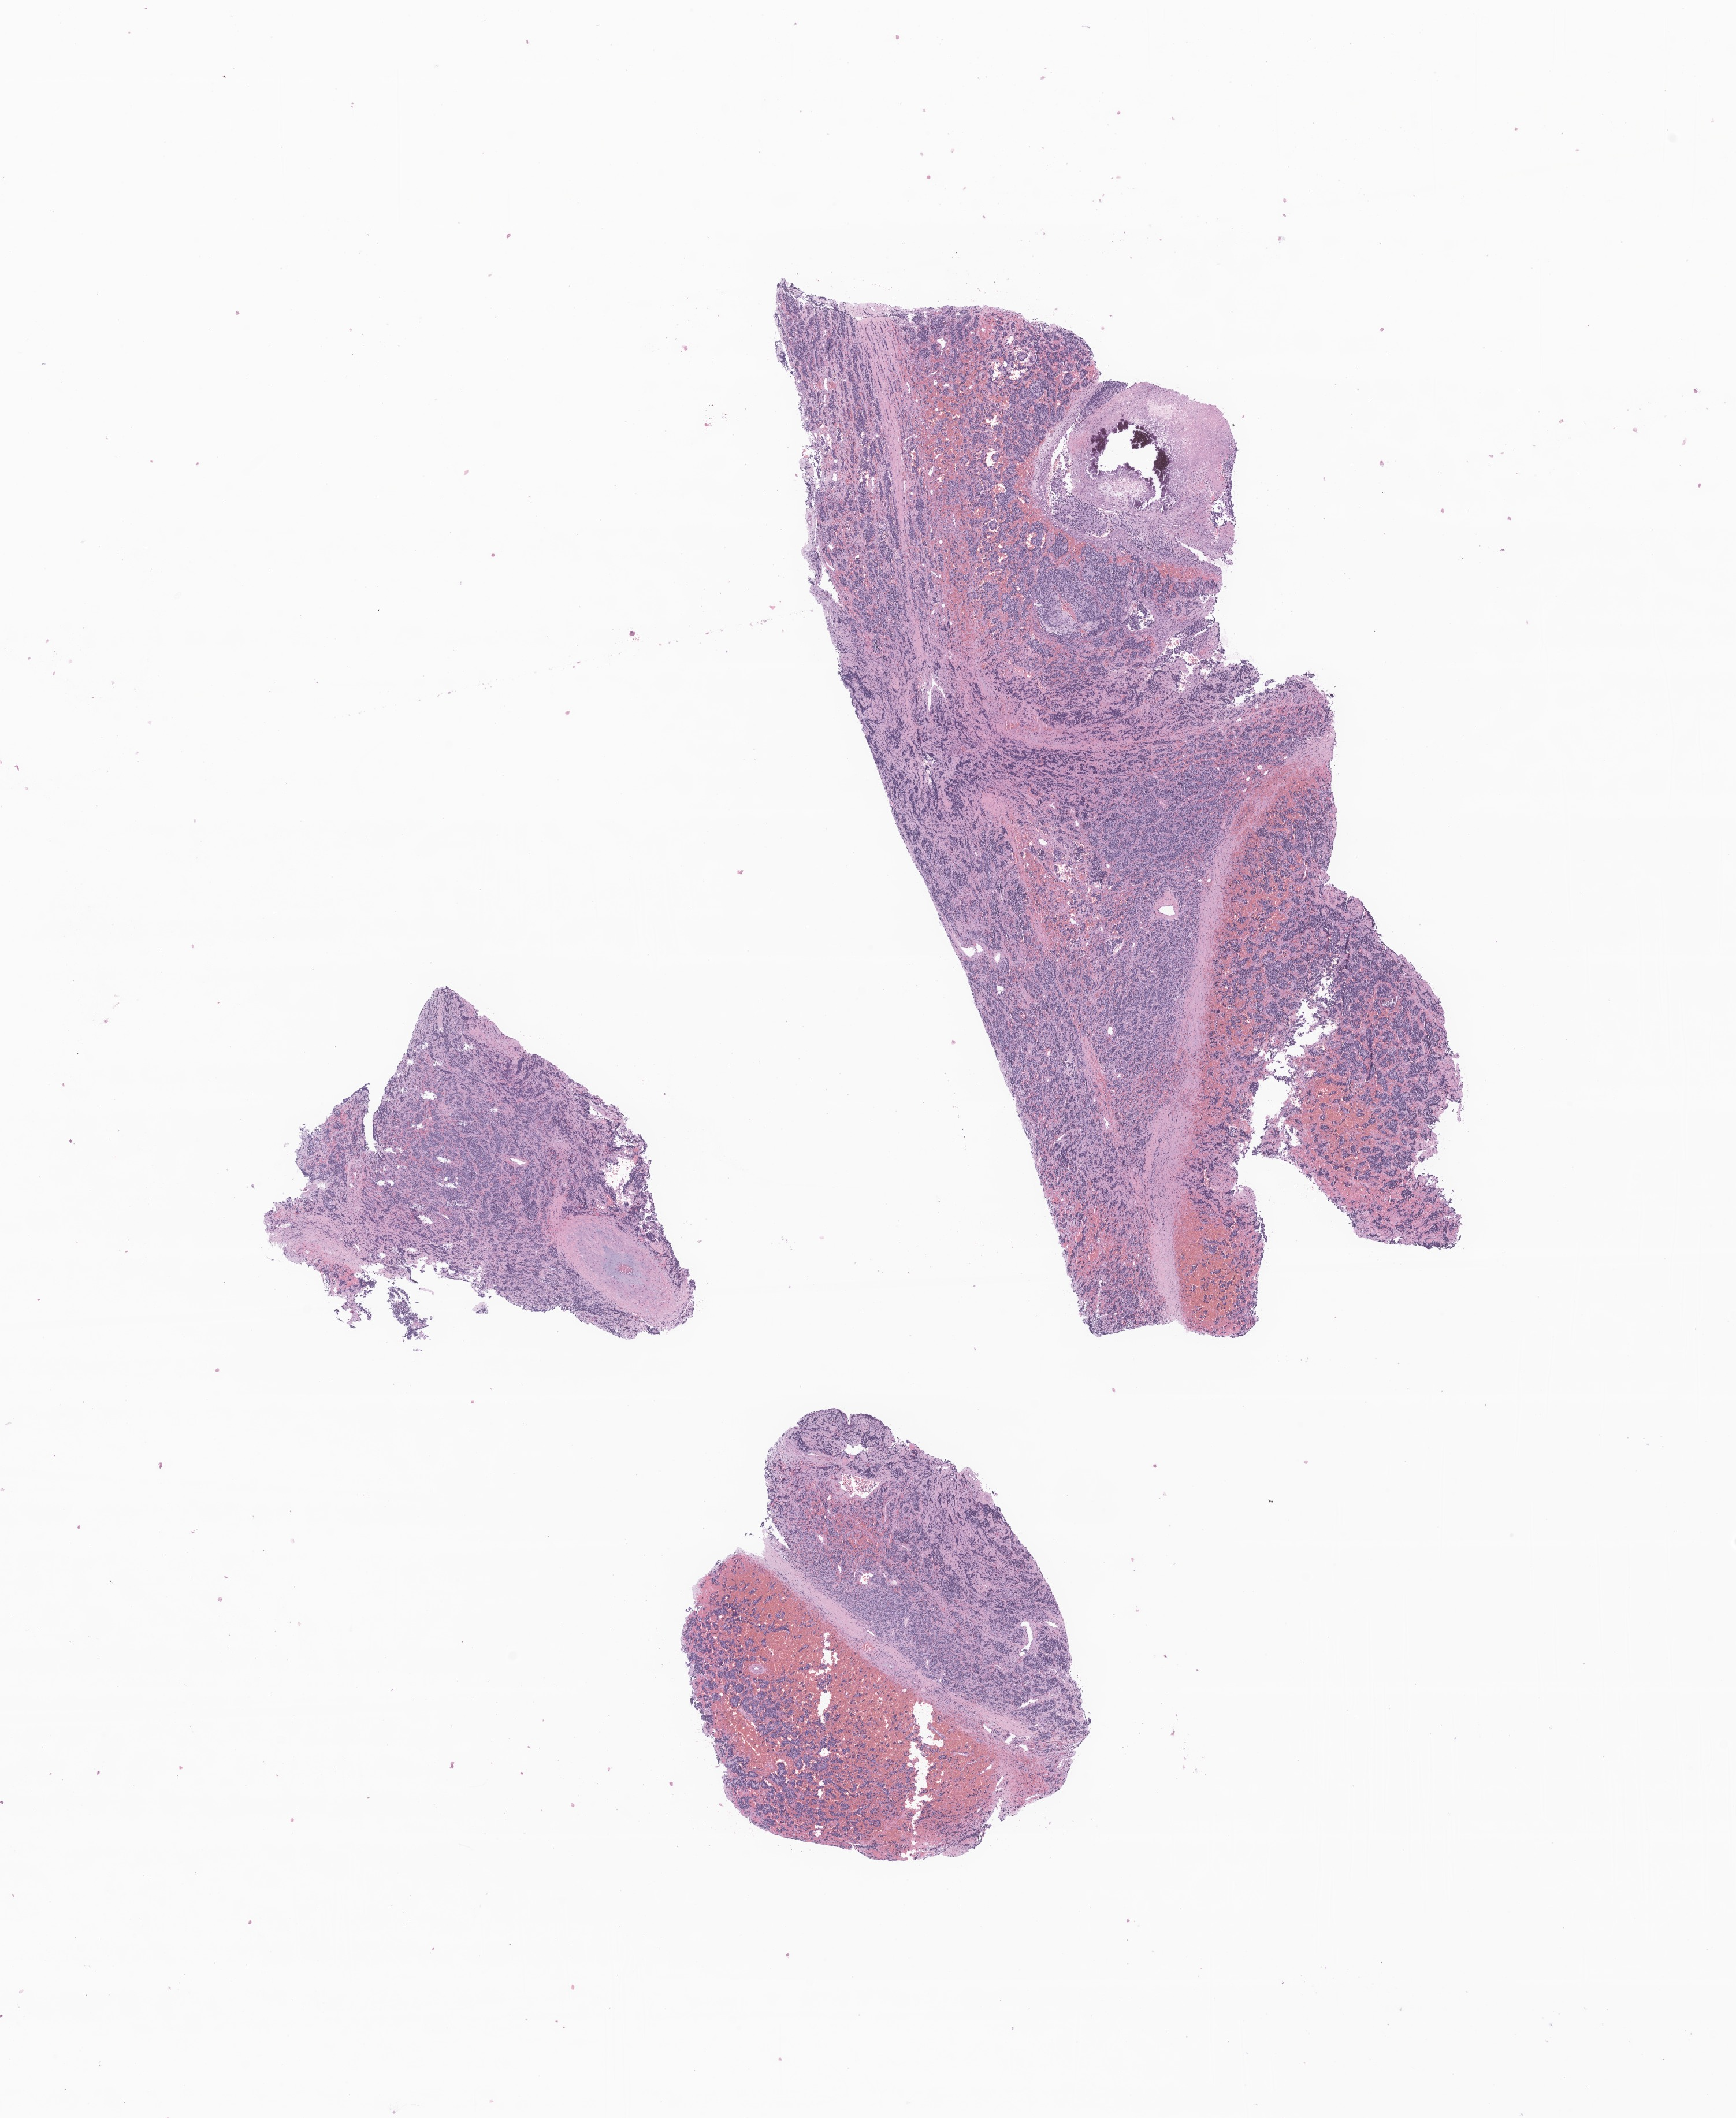
Digitized H&E-stained section of tumor tissue from the abdomen, whole scanned area (about 12.7 x 15.5 mm) shown as a low-resolution overview. FFPE section. Patient female; age 474 days (about 1.3 years).
Diagnosis (ICD-O-3 morphology term): Neuroblastoma, NOS.